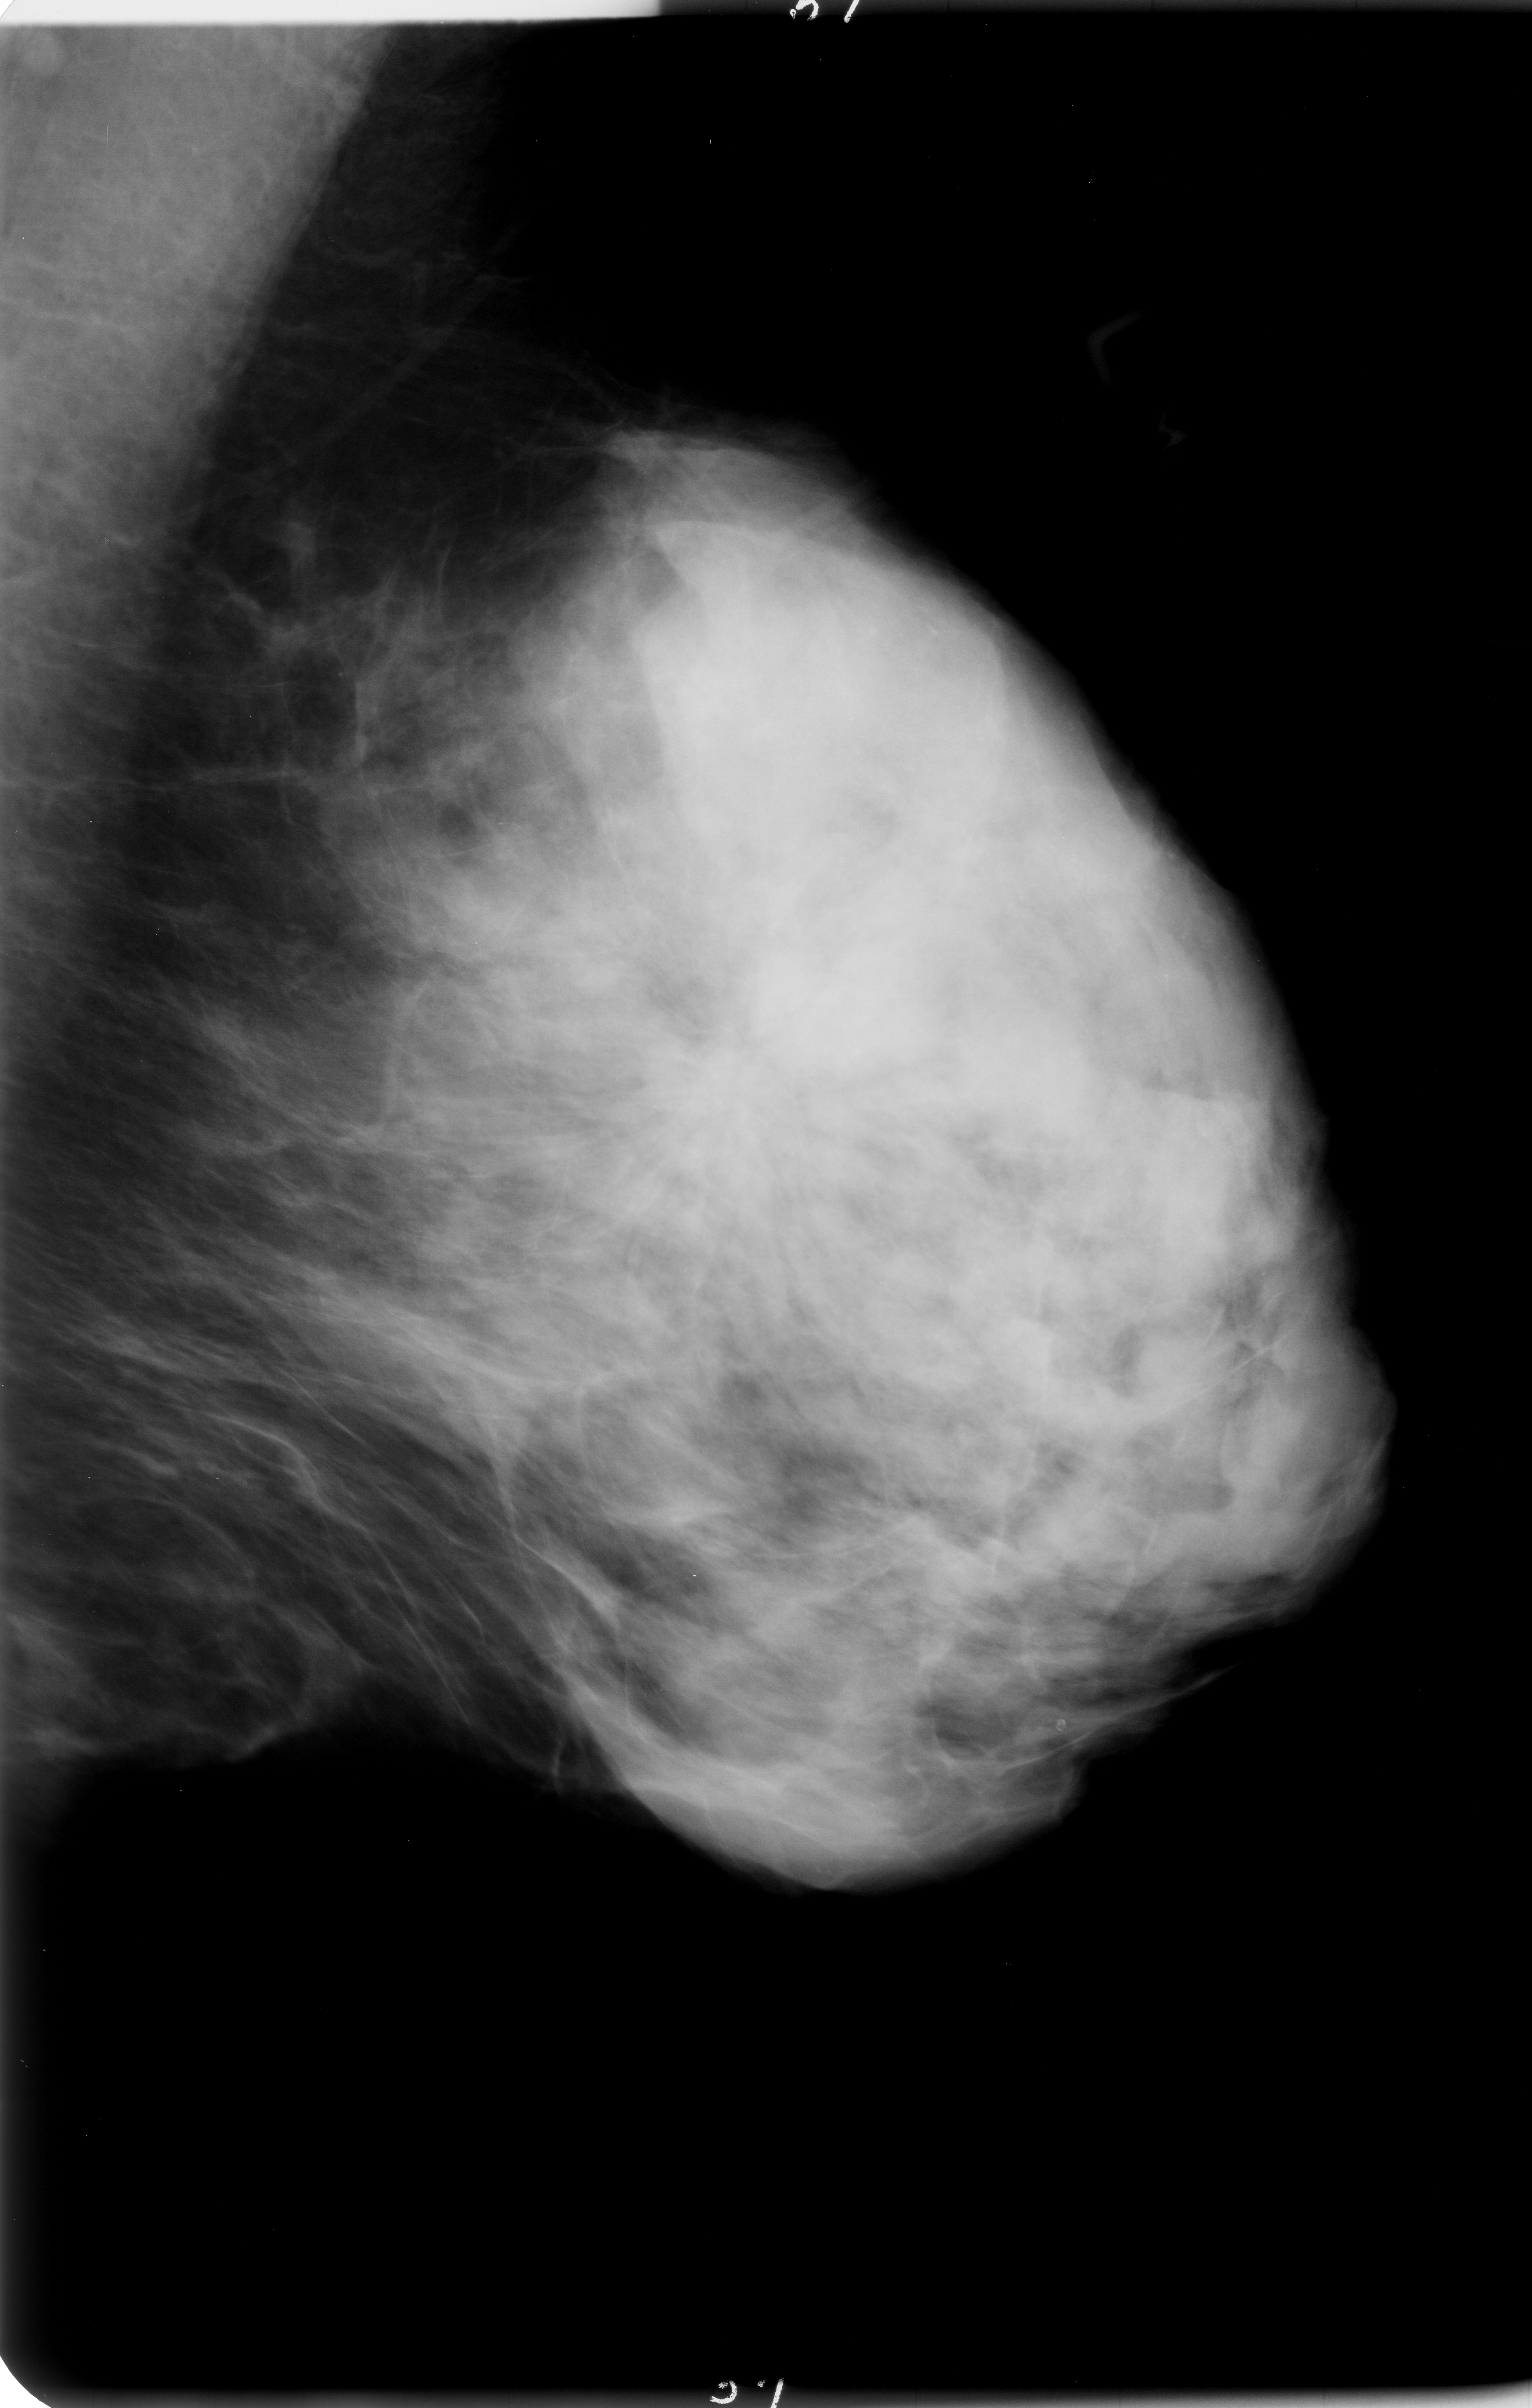
Scanned film-screen mammogram, left breast, mediolateral oblique (MLO) view, BI-RADS breast density category 4 (scale 1–4).
Marked findings (only marked abnormalities are described; nothing is implied about the rest of the image): calcifications, morphology pleomorphic, distribution clustered; BI-RADS assessment category 5; subtlety rating 3 on a 1 (subtle) to 5 (obvious) scale; pathology (as recorded): malignant.